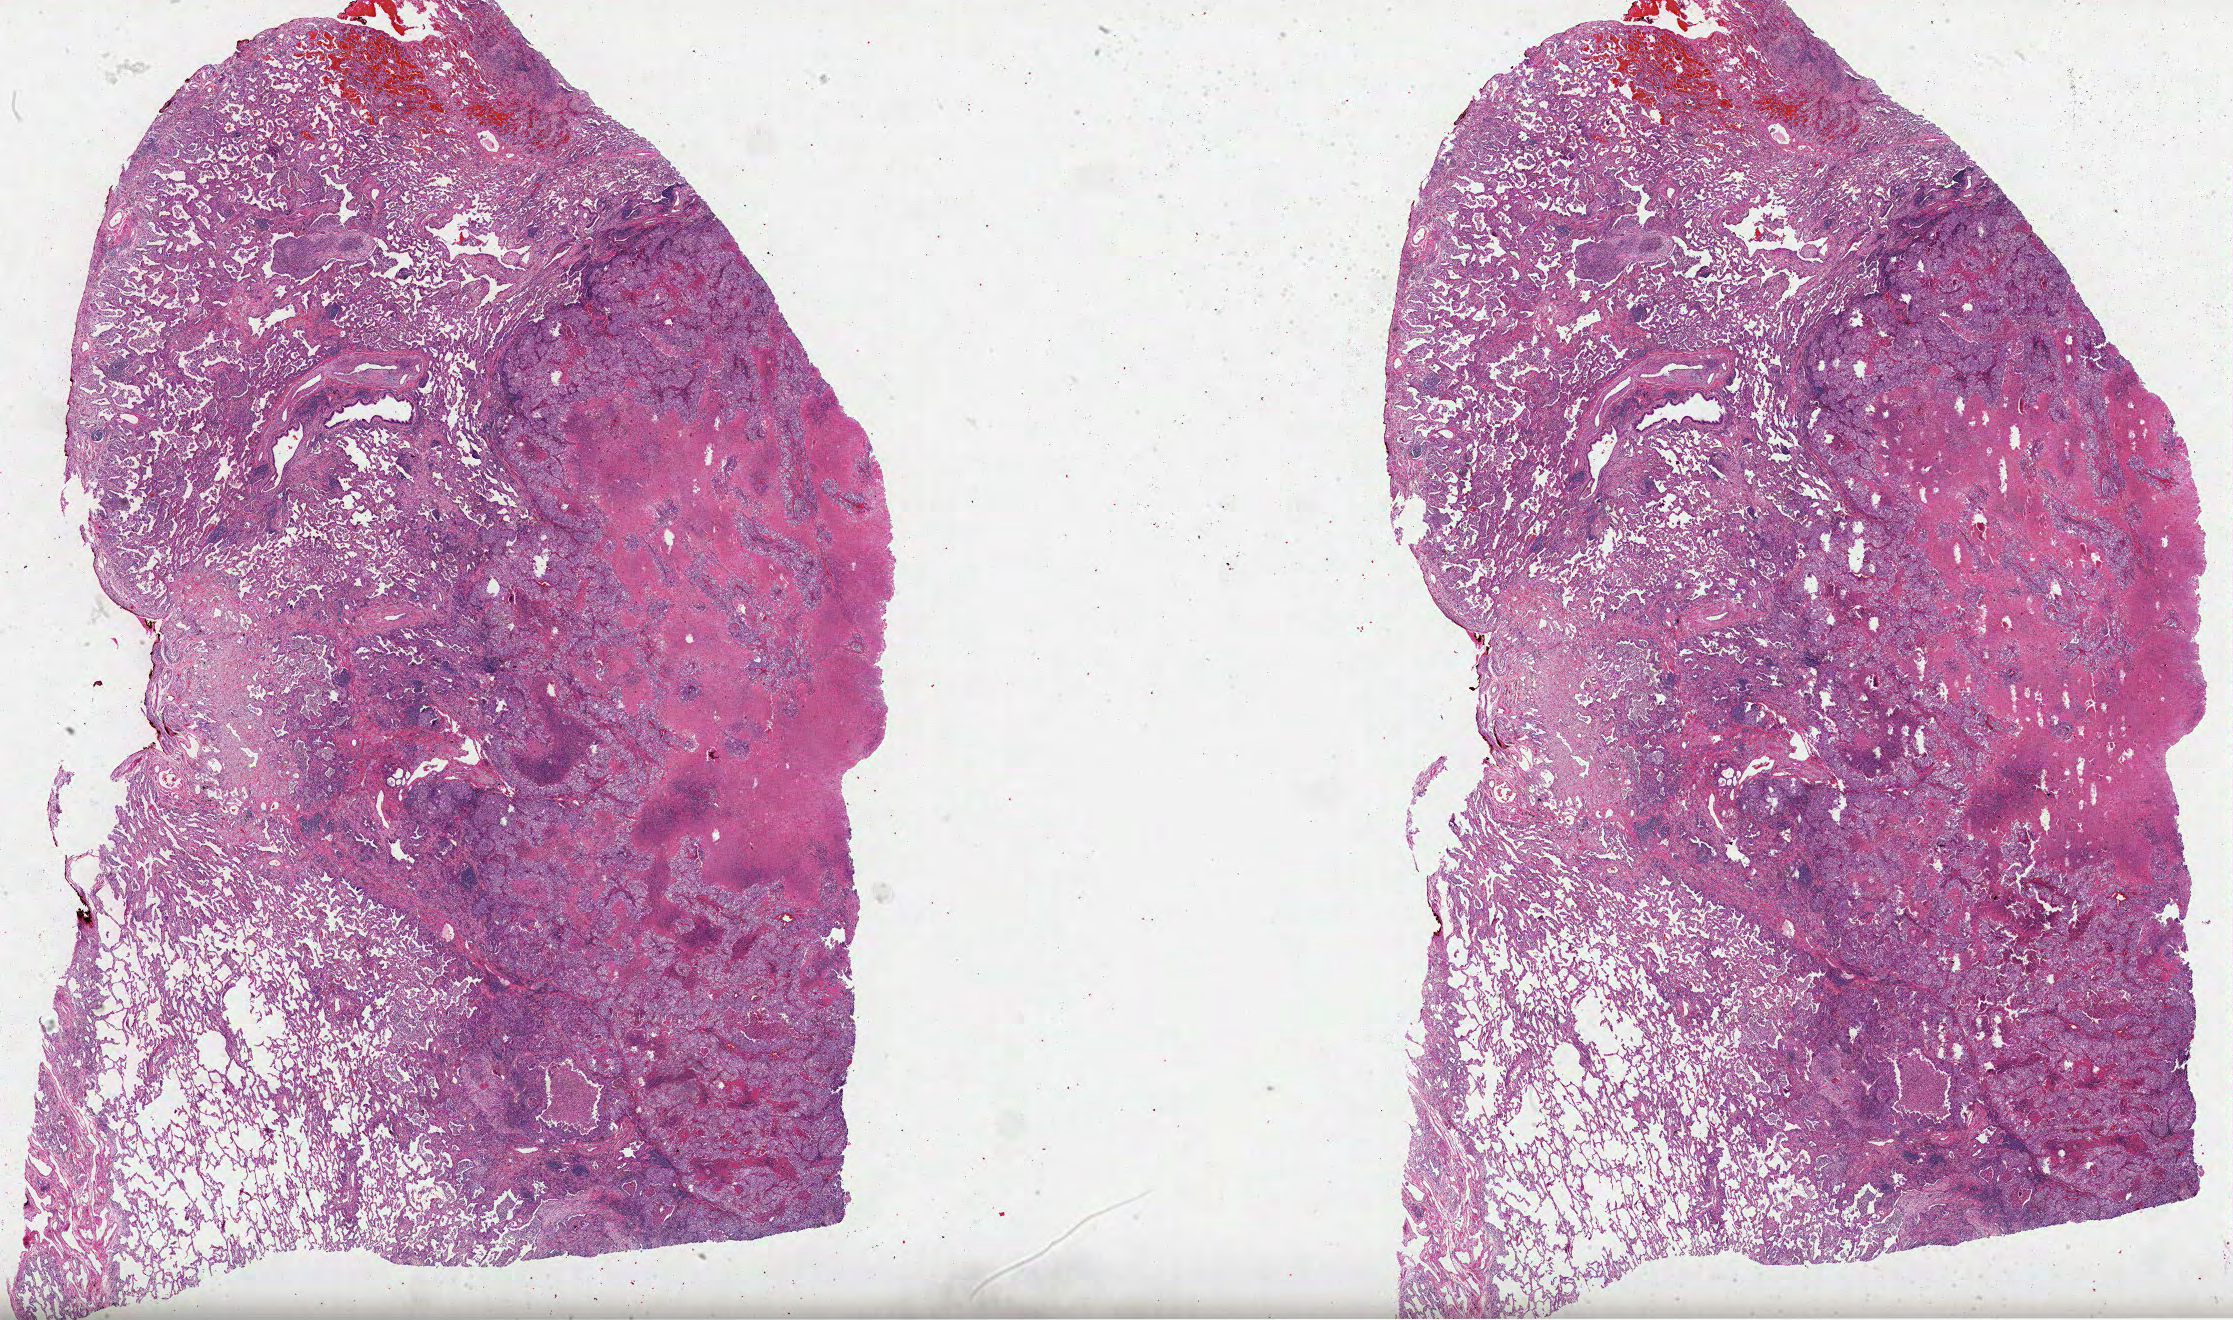
Whole-slide histology image, H&E — shown as a low-resolution overview of the whole scanned area (about 36.0 x 21.3 mm), FFPE section, sample: primary tumour, lung. Patient: female, age at initial diagnosis 81 years.
* AJCC pathologic stage: IIIA (7th edition)
* pathologic diagnosis: Clear cell adenocarcinoma, NOS